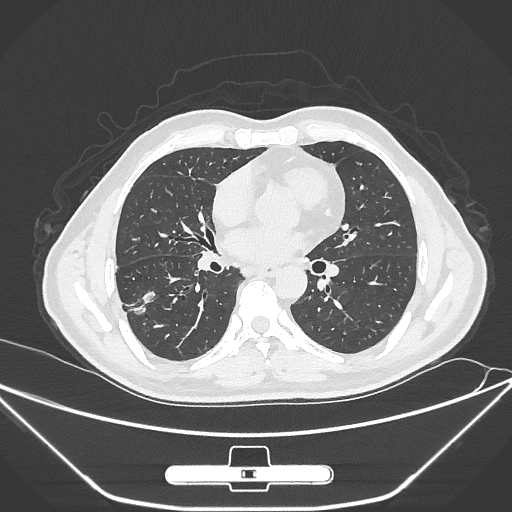
Chest CT, one axial slice. Slice 141 of 310 in the series (ordered by position). 120 kVp. Lung window (W 1500 / L -600 HU). 512 × 512 image matrix, field of view 398 × 398 mm. Patient: male, 71 years. From the clinical record (not read from this slice): clinical TNM (as recorded): T1c N0 M0; histopathological grade: G2.
Annotated regions visible in this slice (rectangle marked by the reading radiologist):
- lung tumour (recorded histology: adenocarcinoma): bounding box <127,283,162,324> (left, top, right, bottom; pixels)